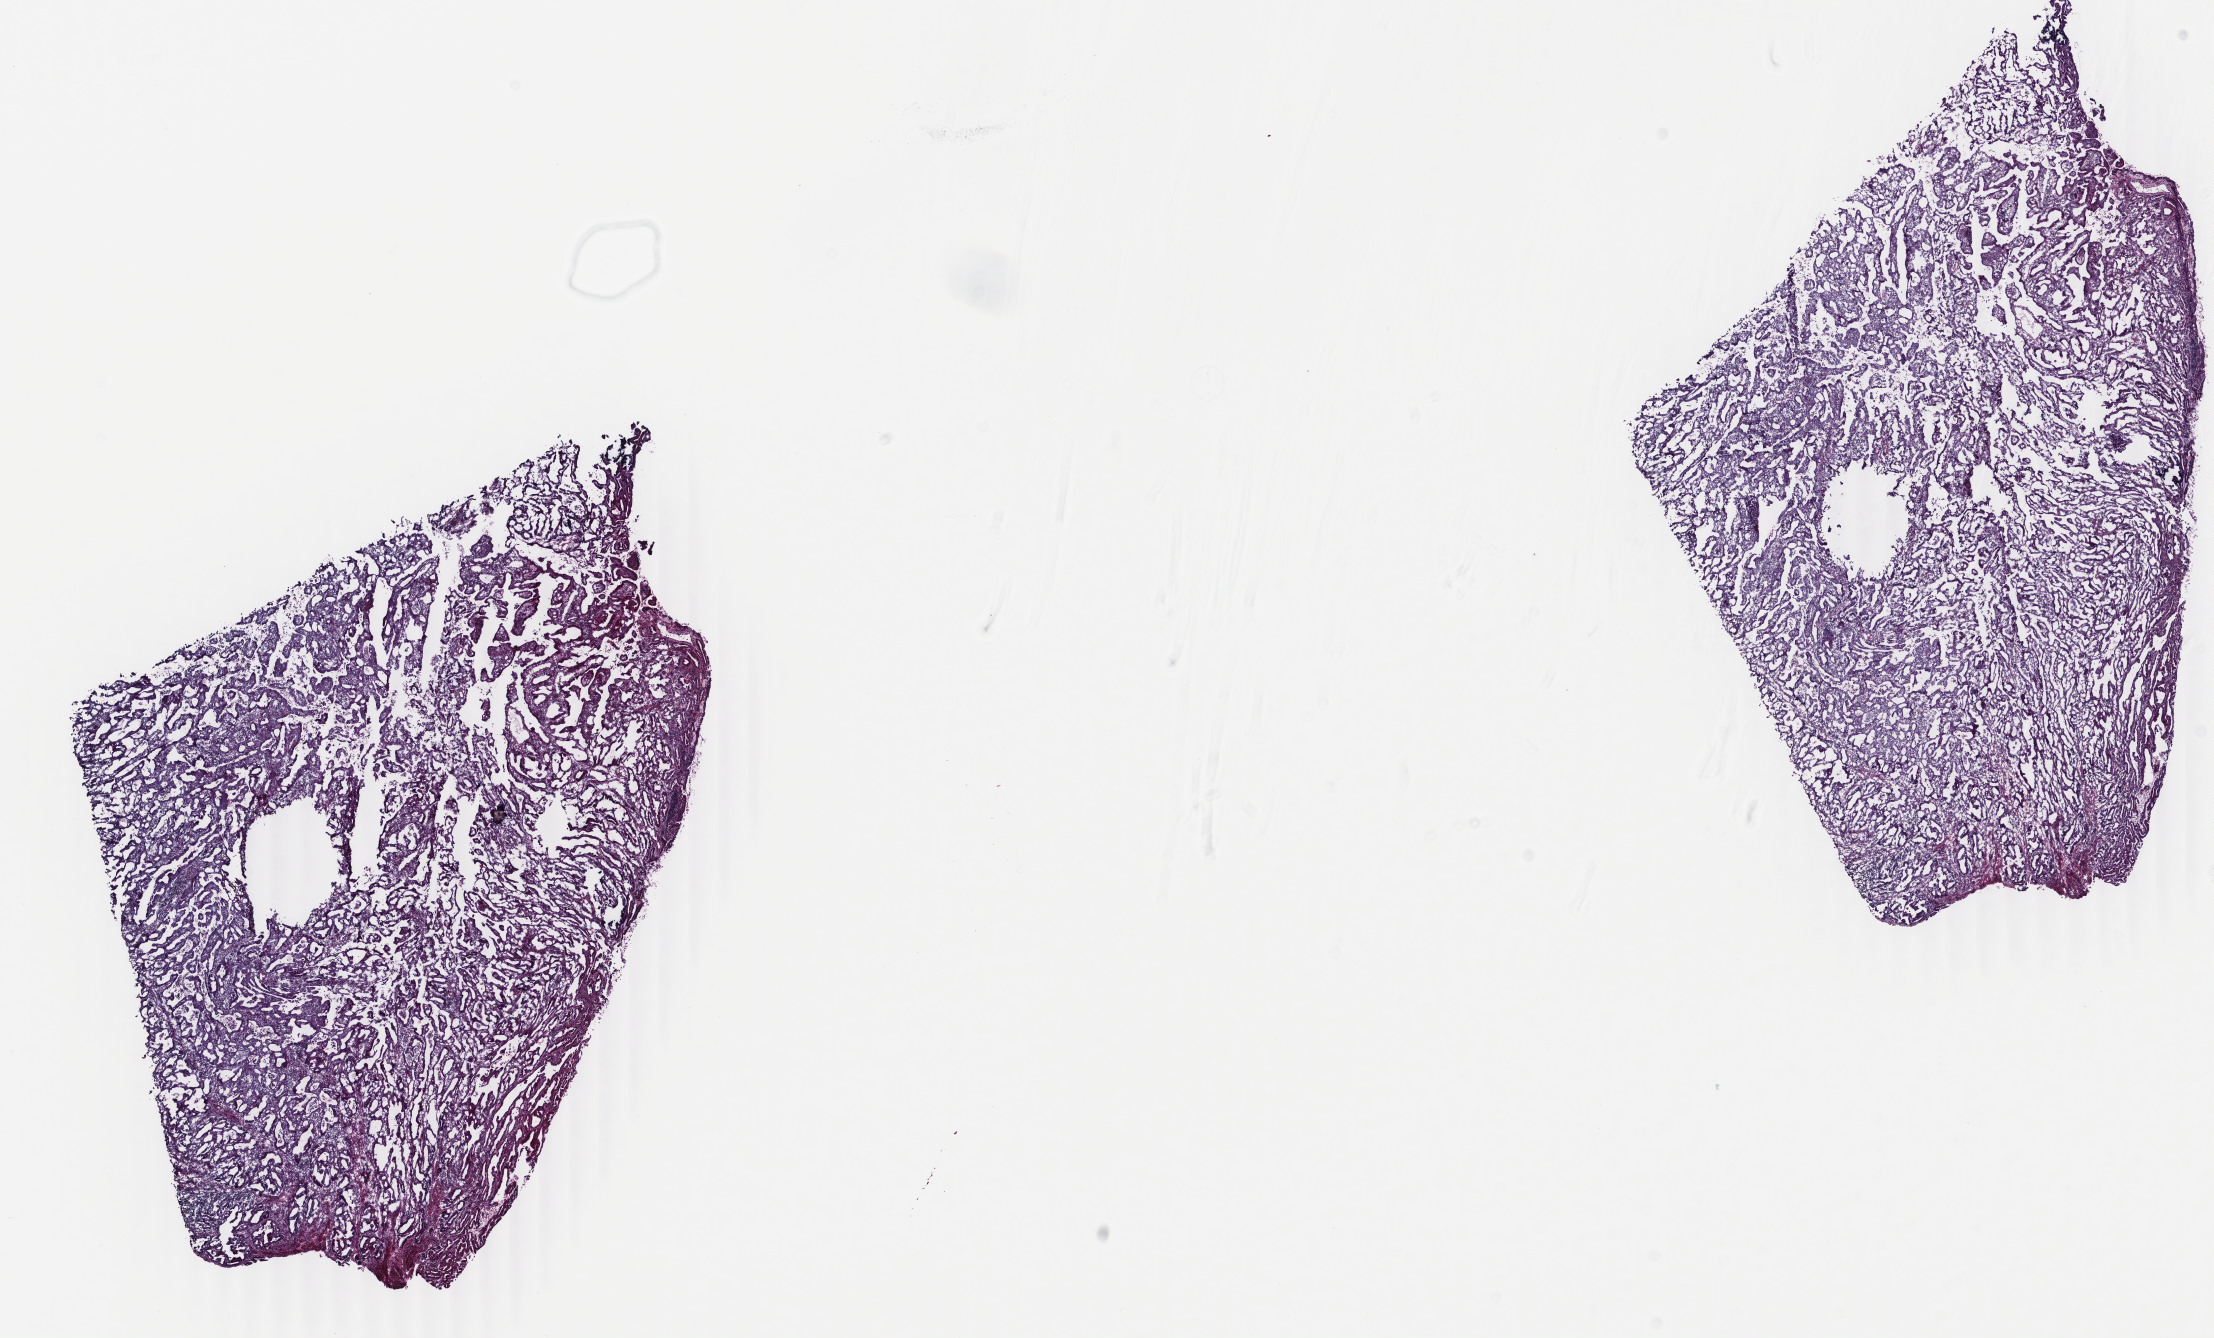
Whole-slide histology image, H&E-stained, low-resolution overview of the scanned area, about 17.6 x 10.6 mm (acquisition: 40x scan), frozen section from the top of the tissue portion, uterus, primary tumour sample. Female patient; age at initial diagnosis 58 years. Pathologist review of this section (percent, as recorded): tumour cells 70%, tumour nuclei 80%.
Histologic diagnosis: Endometrioid adenocarcinoma, NOS (endometrium).